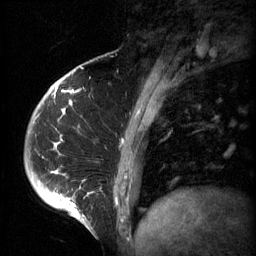
Breast MRI (dynamic contrast-enhanced), one sagittal slice. Position 16 of 60 along the scan axis. 3 images stored at this slice position (order not interpretable as contrast timing). 1.5 T. TE 4.2 ms, TR 11 ms. 2 mm slice thickness. 256 × 256 image matrix, field of view 200 × 200 mm. Patient: female, 51 years.
Annotated regions visible in this slice (semi-automatically segmented with operator editing):
- analysis volume of interest (the breast-tissue region the enhancement analysis was run in; not a lesion): bounding box <48,82,161,197> (left, top, right, bottom; pixels)
- tumour enhancement mask (voxels above the 70 % enhancement threshold inside the analysis volume of interest): <48,82,153,197>